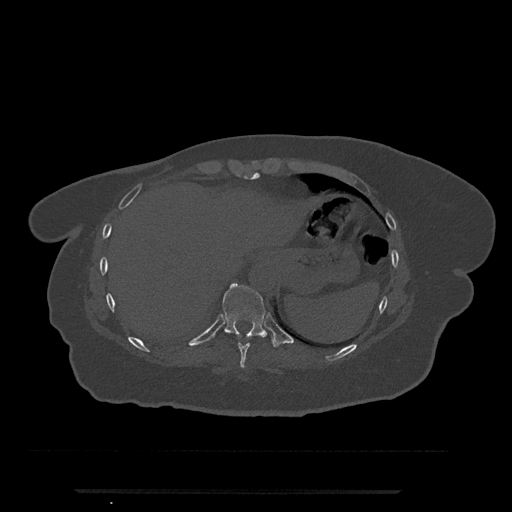
CT including the spine, one axial slice. Position 308 of 797 along the scan axis. Reconstruction kernel Br40s/3. 120 kVp. Bone window (W 1800 / L 400 HU). 0.5 mm slice thickness. 512 × 512 image matrix, field of view 440 × 440 mm. Patient: female, 51 years. Case-level facts recorded for this patient, not image findings: primary cancer: neuro; vertebrae with lytic lesions (as recorded): T8.
Annotated regions visible in this slice (semi-automatically segmented with operator editing):
- T10 vertebra: box from (x=222, y=283) to (x=277, y=347) px
- T9 vertebra: (x=238, y=342)–(x=250, y=368)